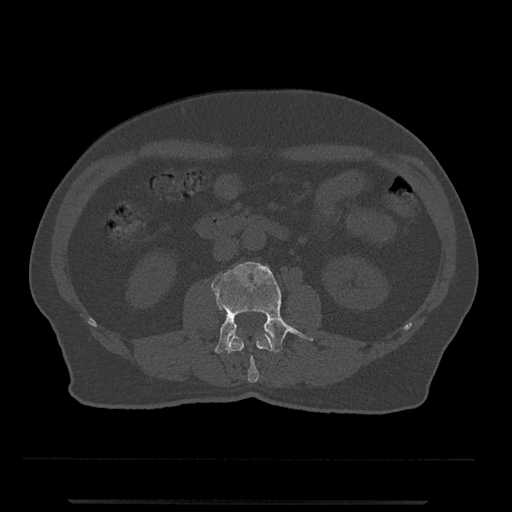
CT including the spine, one axial slice. Slice 224 of 797 in the series (ordered by position). 120 kVp. Bone window (W 1800 / L 400 HU). 512 × 512 image matrix. Patient: male, 63 years. Case-level facts recorded for this patient, not image findings: primary cancer: prostate.
Outlined on this slice (semi-automatic segmentation, software-assisted and operator-edited):
- L2 vertebra: bounding box [x1, y1, x2, y2] px = [227, 333, 274, 383]
- L3 vertebra: [211, 261, 313, 354]